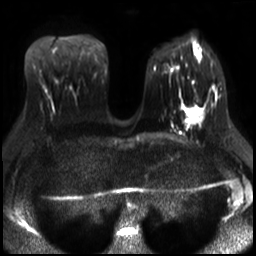
Breast MRI, one axial slice; slice 14 of 30 in the series (ordered by position); diffusion-weighted series; image 2 of 4 stored at this slice position (different b-values; order by instance number); 3 T; 4 mm slice thickness; 256 × 256 image matrix. Female patient.
Annotated regions visible in this slice (outlined manually by an expert reader):
- tumour on diffusion-weighted imaging: bounding box (x1, y1, x2, y2) in pixels: (186, 107, 201, 121)